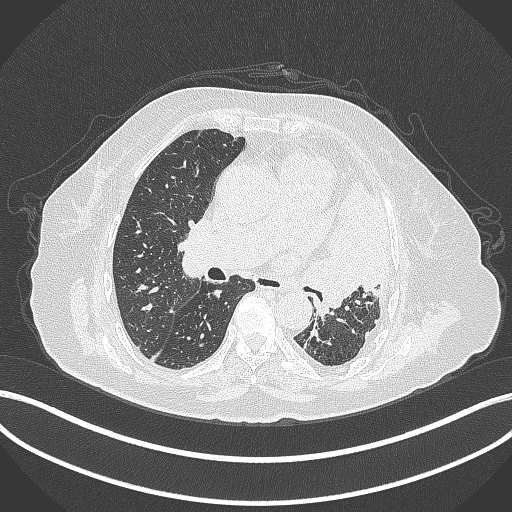
Chest CT, one axial slice. Slice 207 of 399 in the series (ordered by position). Reconstruction kernel B70f. 120 kVp. Lung window (W 1500 / L -600 HU). 1 mm slice thickness. 512 × 512 image matrix, field of view 400 × 400 mm. Patient: female, 75 years. Case-level facts recorded for this patient, not image findings: clinical TNM (as recorded): T3 N3 M1.
Outlined on this slice (bounding box drawn by a radiologist):
- lung tumour (recorded histology: adenocarcinoma): bounding box (x1, y1, x2, y2) in pixels: (301, 177, 392, 315)